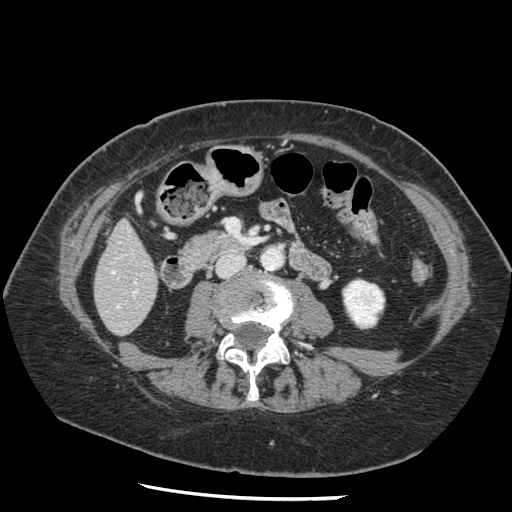
Contrast-enhanced abdominal CT, one axial slice; slice 34 of 148 in the series (ordered by position); reconstruction kernel STANDARD; intravenous contrast given; soft-tissue window (W 400 / L 40 HU); 2.5 mm slice thickness; 512 × 512 image matrix. Female patient, age 85 years. From the clinical record (not read from this slice): diagnosis: colorectal cancer liver metastases, imaged before liver resection; multiple liver metastases: no; largest metastasis: 0.9 cm; disease in both lobes: no.
Outlined on this slice (expert manual segmentation):
- hepatic veins: box from (x=112, y=271) to (x=118, y=308) px
- liver: (x=95, y=223)–(x=158, y=334)
- planned liver remnant (the part of the liver to remain after resection): (x=95, y=223)–(x=158, y=332)